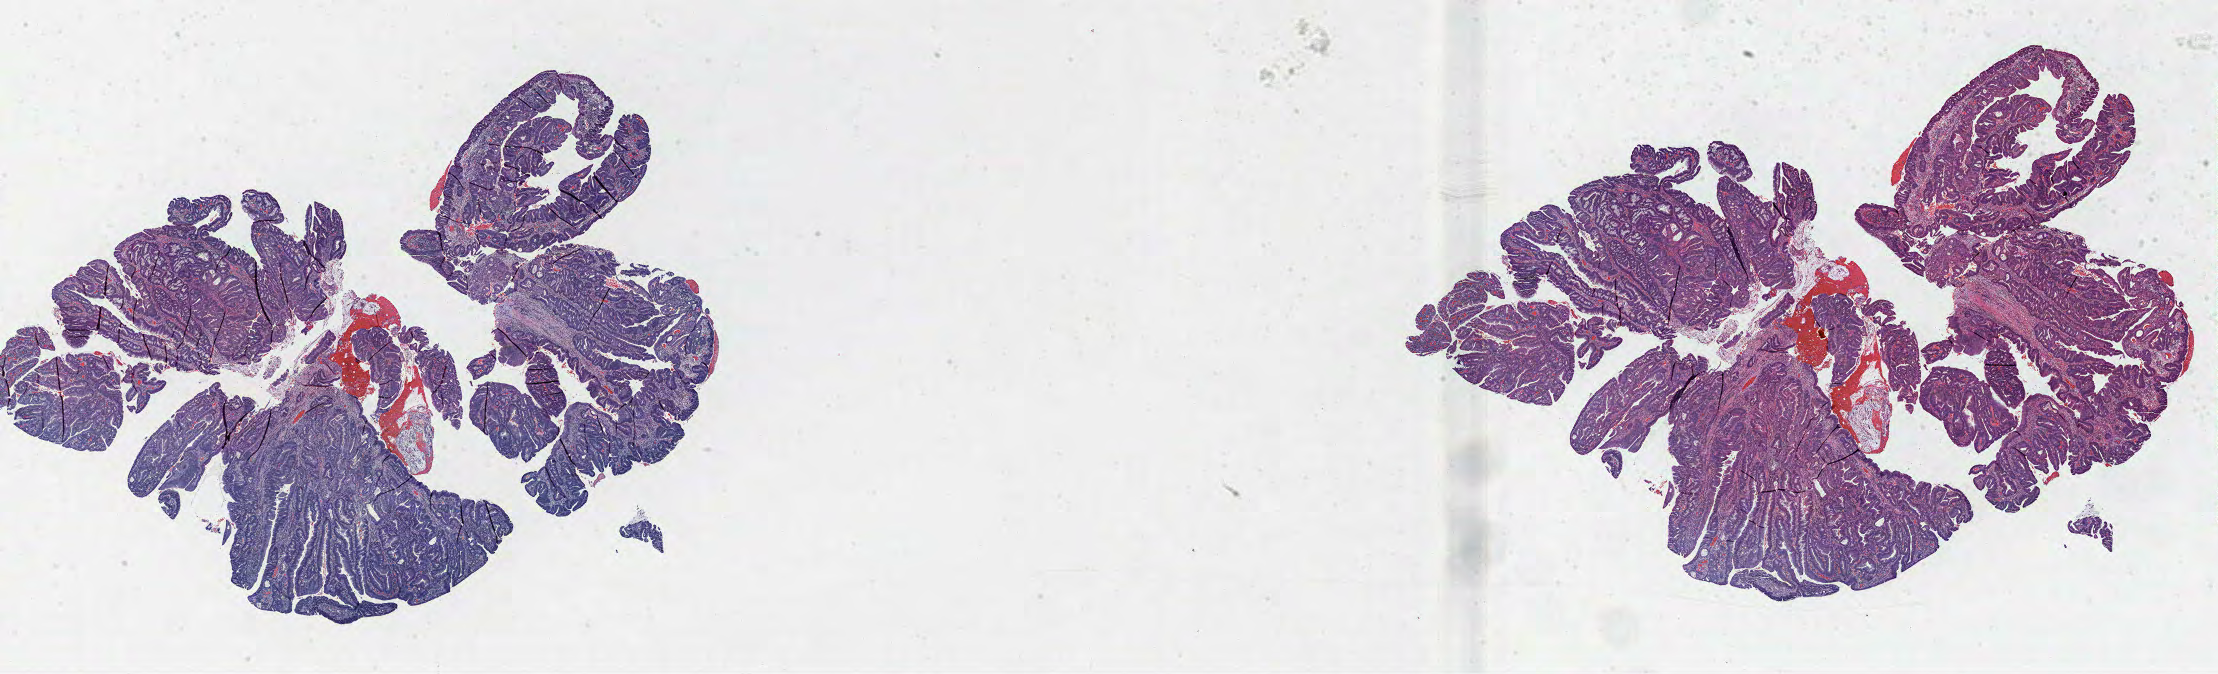
H&E-stained whole-slide image, shown as a low-resolution overview of the whole scanned area (about 35.8 x 10.9 mm); formalin-fixed paraffin-embedded (FFPE) diagnostic section; primary tumour sample from the colon. Male patient; age at initial diagnosis 80 years.
Diagnosis: Adenocarcinoma, NOS (ascending colon). AJCC pathologic stage: IIIC. TNM: T4a N2a MX.